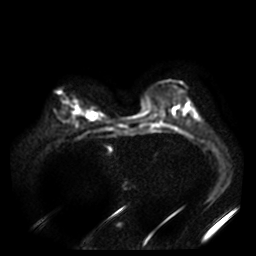
Breast MRI, one axial slice. Position 13 of 40 along the scan axis. Diffusion-weighted series; image 2 of 4 stored at this slice position (different b-values; order by instance number). 3 T. 256 × 256 image matrix. Female patient.
Structures marked on this image (manually delineated by an expert):
- tumour on diffusion-weighted imaging: bounding box (x1, y1, x2, y2) in pixels: (74, 110, 95, 119)